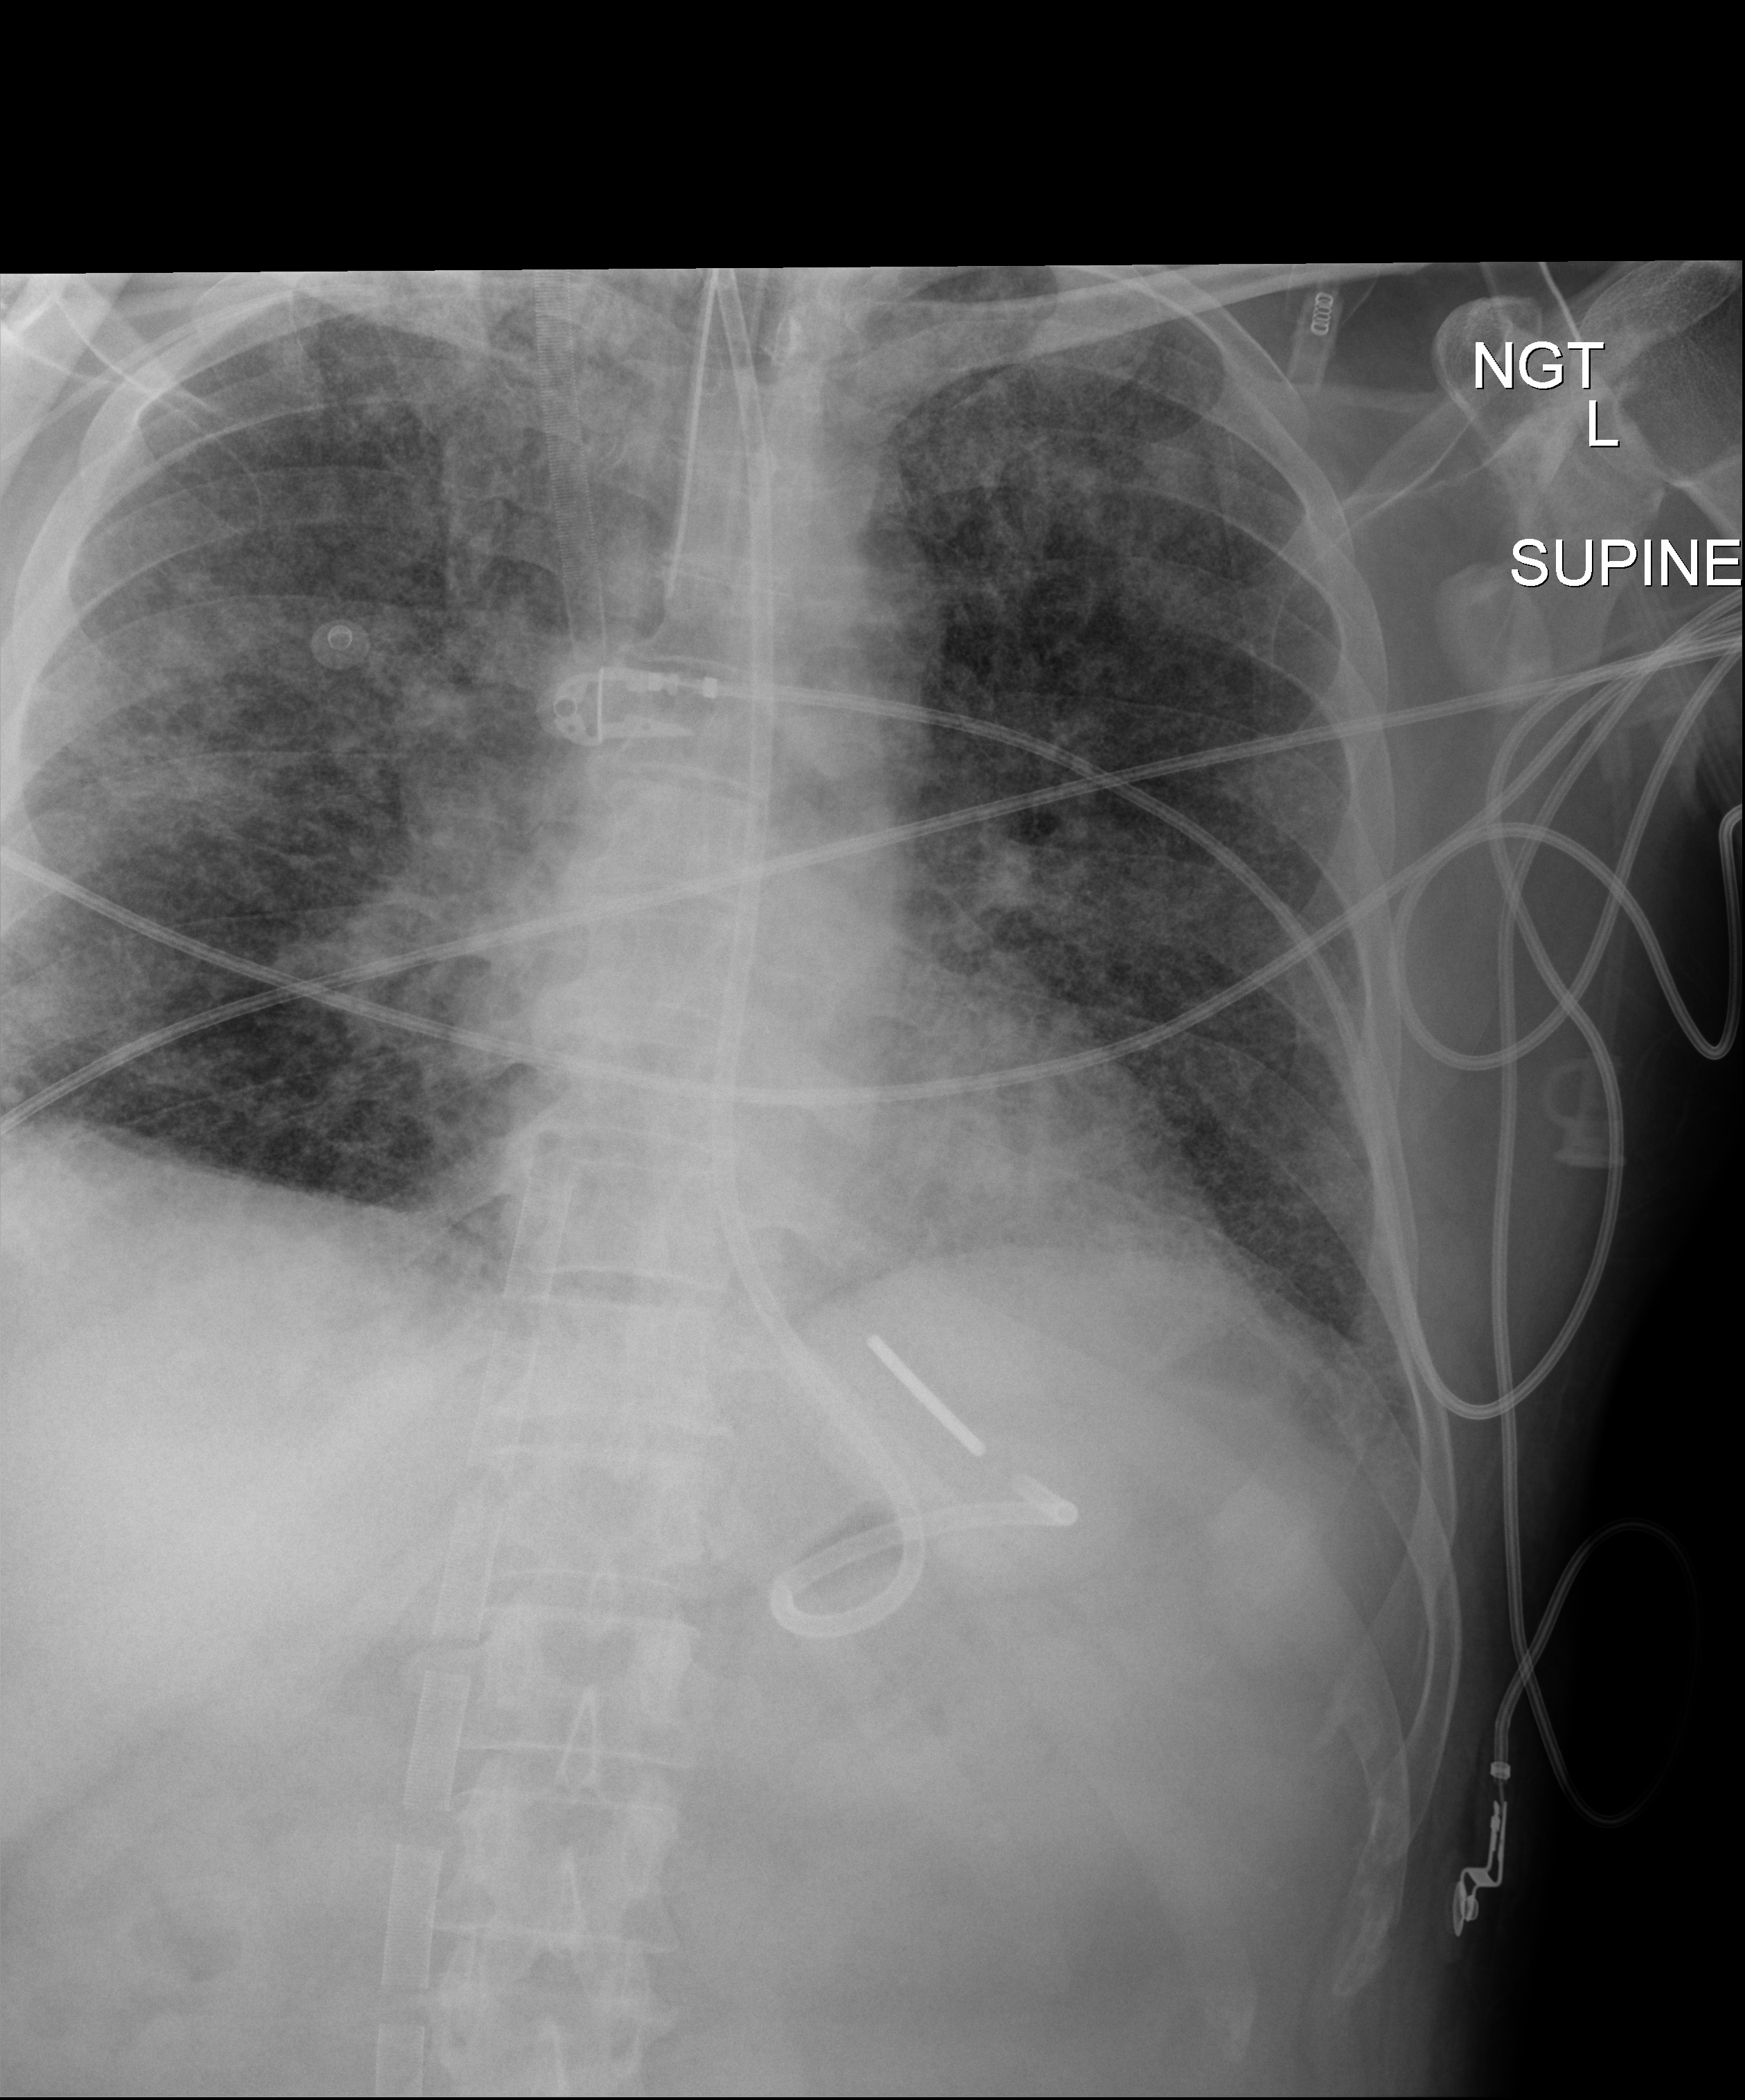
Bedside chest radiograph (digital radiography), anteroposterior (AP) projection. Male patient hospitalised with COVID-19, age 18–59 years.
Admission-level facts for this patient (not findings on this image; timing relative to this image not recorded):
- chronic kidney disease (admission record): no